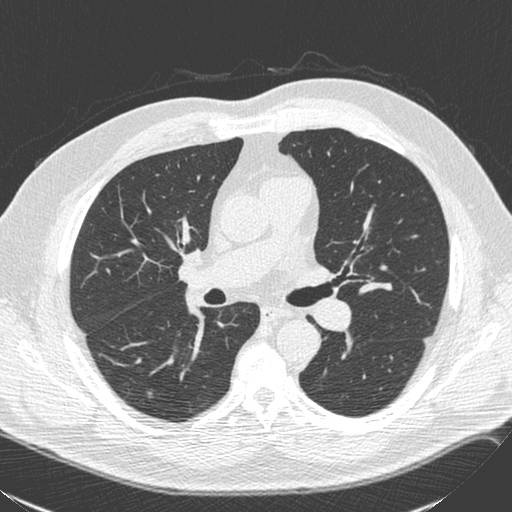
Chest CT (low-dose screening protocol), one axial image; baseline screening round; lung window (W 1500 / L -600 HU); 1.3 mm slice thickness; 120 kVp; slice 99 of 248 in the series; 512 × 512 image matrix. Male participant, aged 71 years at enrolment. Former smoker at enrolment.
• Expert reader's lesion annotation, box from (x=133, y=380) to (x=167, y=409) px.
• Screening reader's record for this exam (one nodule recorded; not confirmed to be the boxed lesion): non-calcified nodule or mass ≥4 mm, right lower lobe, 6 × 6 mm, smooth margins, soft tissue attenuation.
• Participant outcome: lung cancer diagnosed 231 days after this screen — squamous cell carcinoma, NOS, right lower lobe, poorly differentiated (G3), stage IA (AJCC 6th edition), 4 mm at pathology.